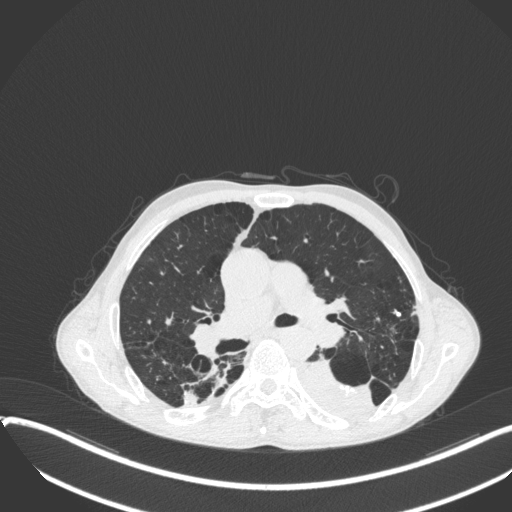
Chest CT, one axial slice; slice 230 of 400 in the series (ordered by position); 120 kVp; lung window (W 1500 / L -600 HU); 1 mm slice thickness; 512 × 512 image matrix, field of view 400 × 400 mm. Male patient, age 57 years. From the clinical record (not read from this slice): clinical TNM (as recorded): T4 N0 M0.
Outlined on this slice (bounding box drawn by a radiologist):
- lung tumour (recorded histology: squamous cell carcinoma): bounding box <290,358,379,425> (left, top, right, bottom; pixels)